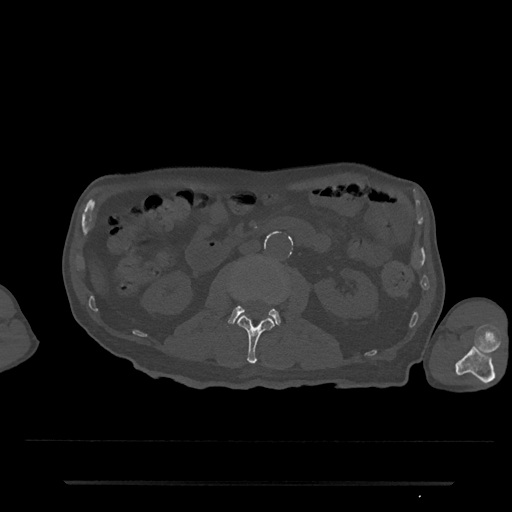
CT including the spine, one axial slice. Slice 31 of 797 in the series (ordered by position). Reconstruction kernel Br40s/3. 120 kVp. Bone window (W 1800 / L 400 HU). 0.5 mm slice thickness. 512 × 512 image matrix. Patient: male, 74 years. From the clinical record (not read from this slice): primary cancer: prostate.
Structures marked on this image (semi-automatically segmented with operator editing):
- L2 vertebra: bounding box [x1, y1, x2, y2] px = [238, 297, 282, 364]
- L3 vertebra: [227, 305, 281, 327]